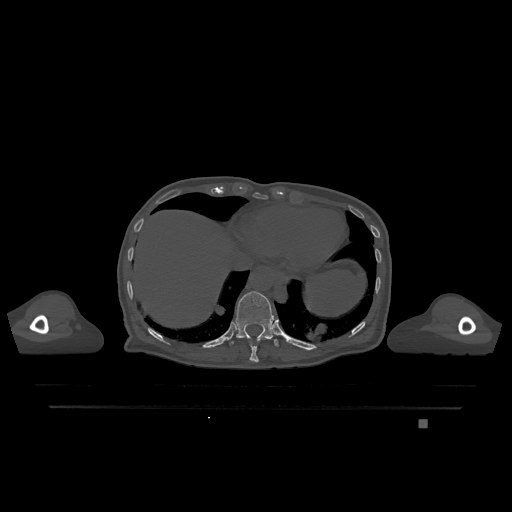
CT including the spine, one axial slice; bone window (W 1800 / L 400 HU); 0.5 mm slice thickness; 512 × 512 image matrix, field of view 500 × 500 mm. Female patient, age 74 years. Case-level facts recorded for this patient, not image findings: primary cancer: lung.
Structures marked on this image (semi-automatic segmentation, software-assisted and operator-edited):
- T10 vertebra: bounding box (x1, y1, x2, y2) in pixels: (249, 342, 259, 363)
- T11 vertebra: (229, 291, 279, 347)